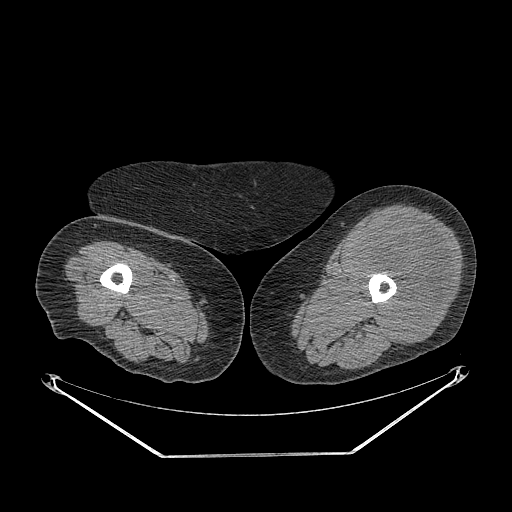
CT of an extremity soft-tissue mass (from a PET/CT study), one axial slice; slice 227 of 267 in the series (ordered by position); reconstruction kernel STANDARD; soft-tissue window (W 400 / L 40 HU); 3.75 mm slice thickness; 512 × 512 image matrix, field of view 500 × 500 mm. Female patient. From the clinical record (not read from this slice): histological type: undifferentiated – high grade; grade: high; site of the primary tumour: left thigh.
Outlined on this slice (expert contour drawn on MRI and transferred to this co-registered scan by the dataset authors):
- gross tumour volume including surrounding oedema: bounding box (x1, y1, x2, y2) in pixels: (354, 215, 453, 341)
- gross tumour volume (mass): (354, 215, 451, 341)